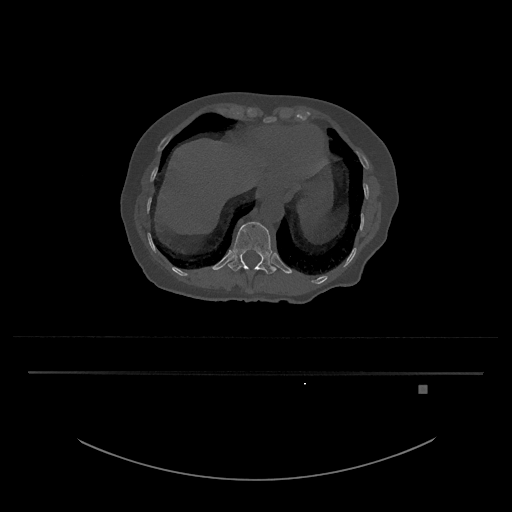
CT including the spine, one axial slice; slice 622 of 797 in the series (ordered by position); reconstruction kernel Br40s/3; 120 kVp; bone window (W 1800 / L 400 HU); 0.5 mm slice thickness; 512 × 512 image matrix, field of view 500 × 500 mm. Patient: female, 57 years. From the clinical record (not read from this slice): primary cancer: cervical.
Annotated regions visible in this slice (semi-automatic segmentation, software-assisted and operator-edited):
- T12 vertebra: bounding box <228,222,277,274> (left, top, right, bottom; pixels)